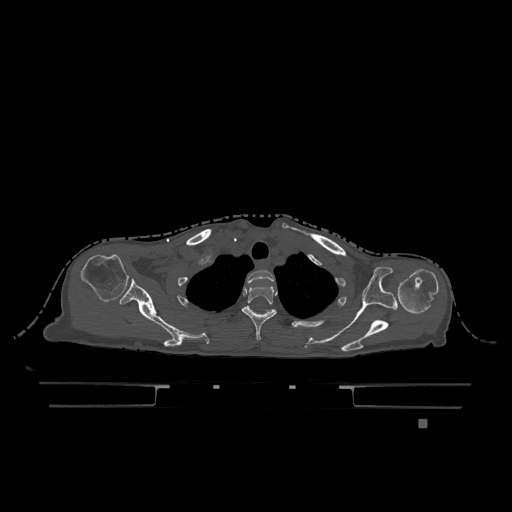
CT including the spine, one axial slice. Position 960 of 1317 along the scan axis. Bone window (W 1800 / L 400 HU). 512 × 512 image matrix, field of view 500 × 500 mm. Patient: female, 74 years. Case-level facts recorded for this patient, not image findings: primary cancer: lung.
Outlined on this slice (semi-automatic segmentation, software-assisted and operator-edited):
- T1 vertebra: bounding box (x1, y1, x2, y2) in pixels: (247, 270, 275, 284)
- T2 vertebra: (241, 285, 277, 341)
- T3 vertebra: (245, 306, 271, 313)